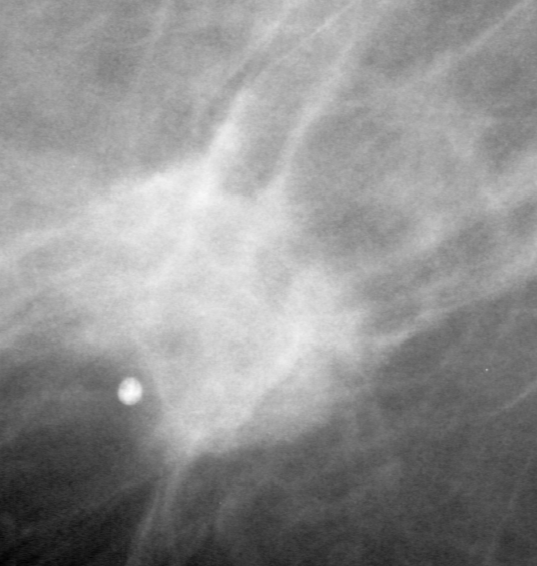
Region of interest cut from a scanned film mammogram (one marked finding), left breast, MLO view, BI-RADS breast density category 1 (scale 1–4).
Mass, shape oval, margins spiculated; BI-RADS assessment category 5; subtlety rating 5 on a 1 (subtle) to 5 (obvious) scale; pathology result (as recorded, not read from the image): malignant.